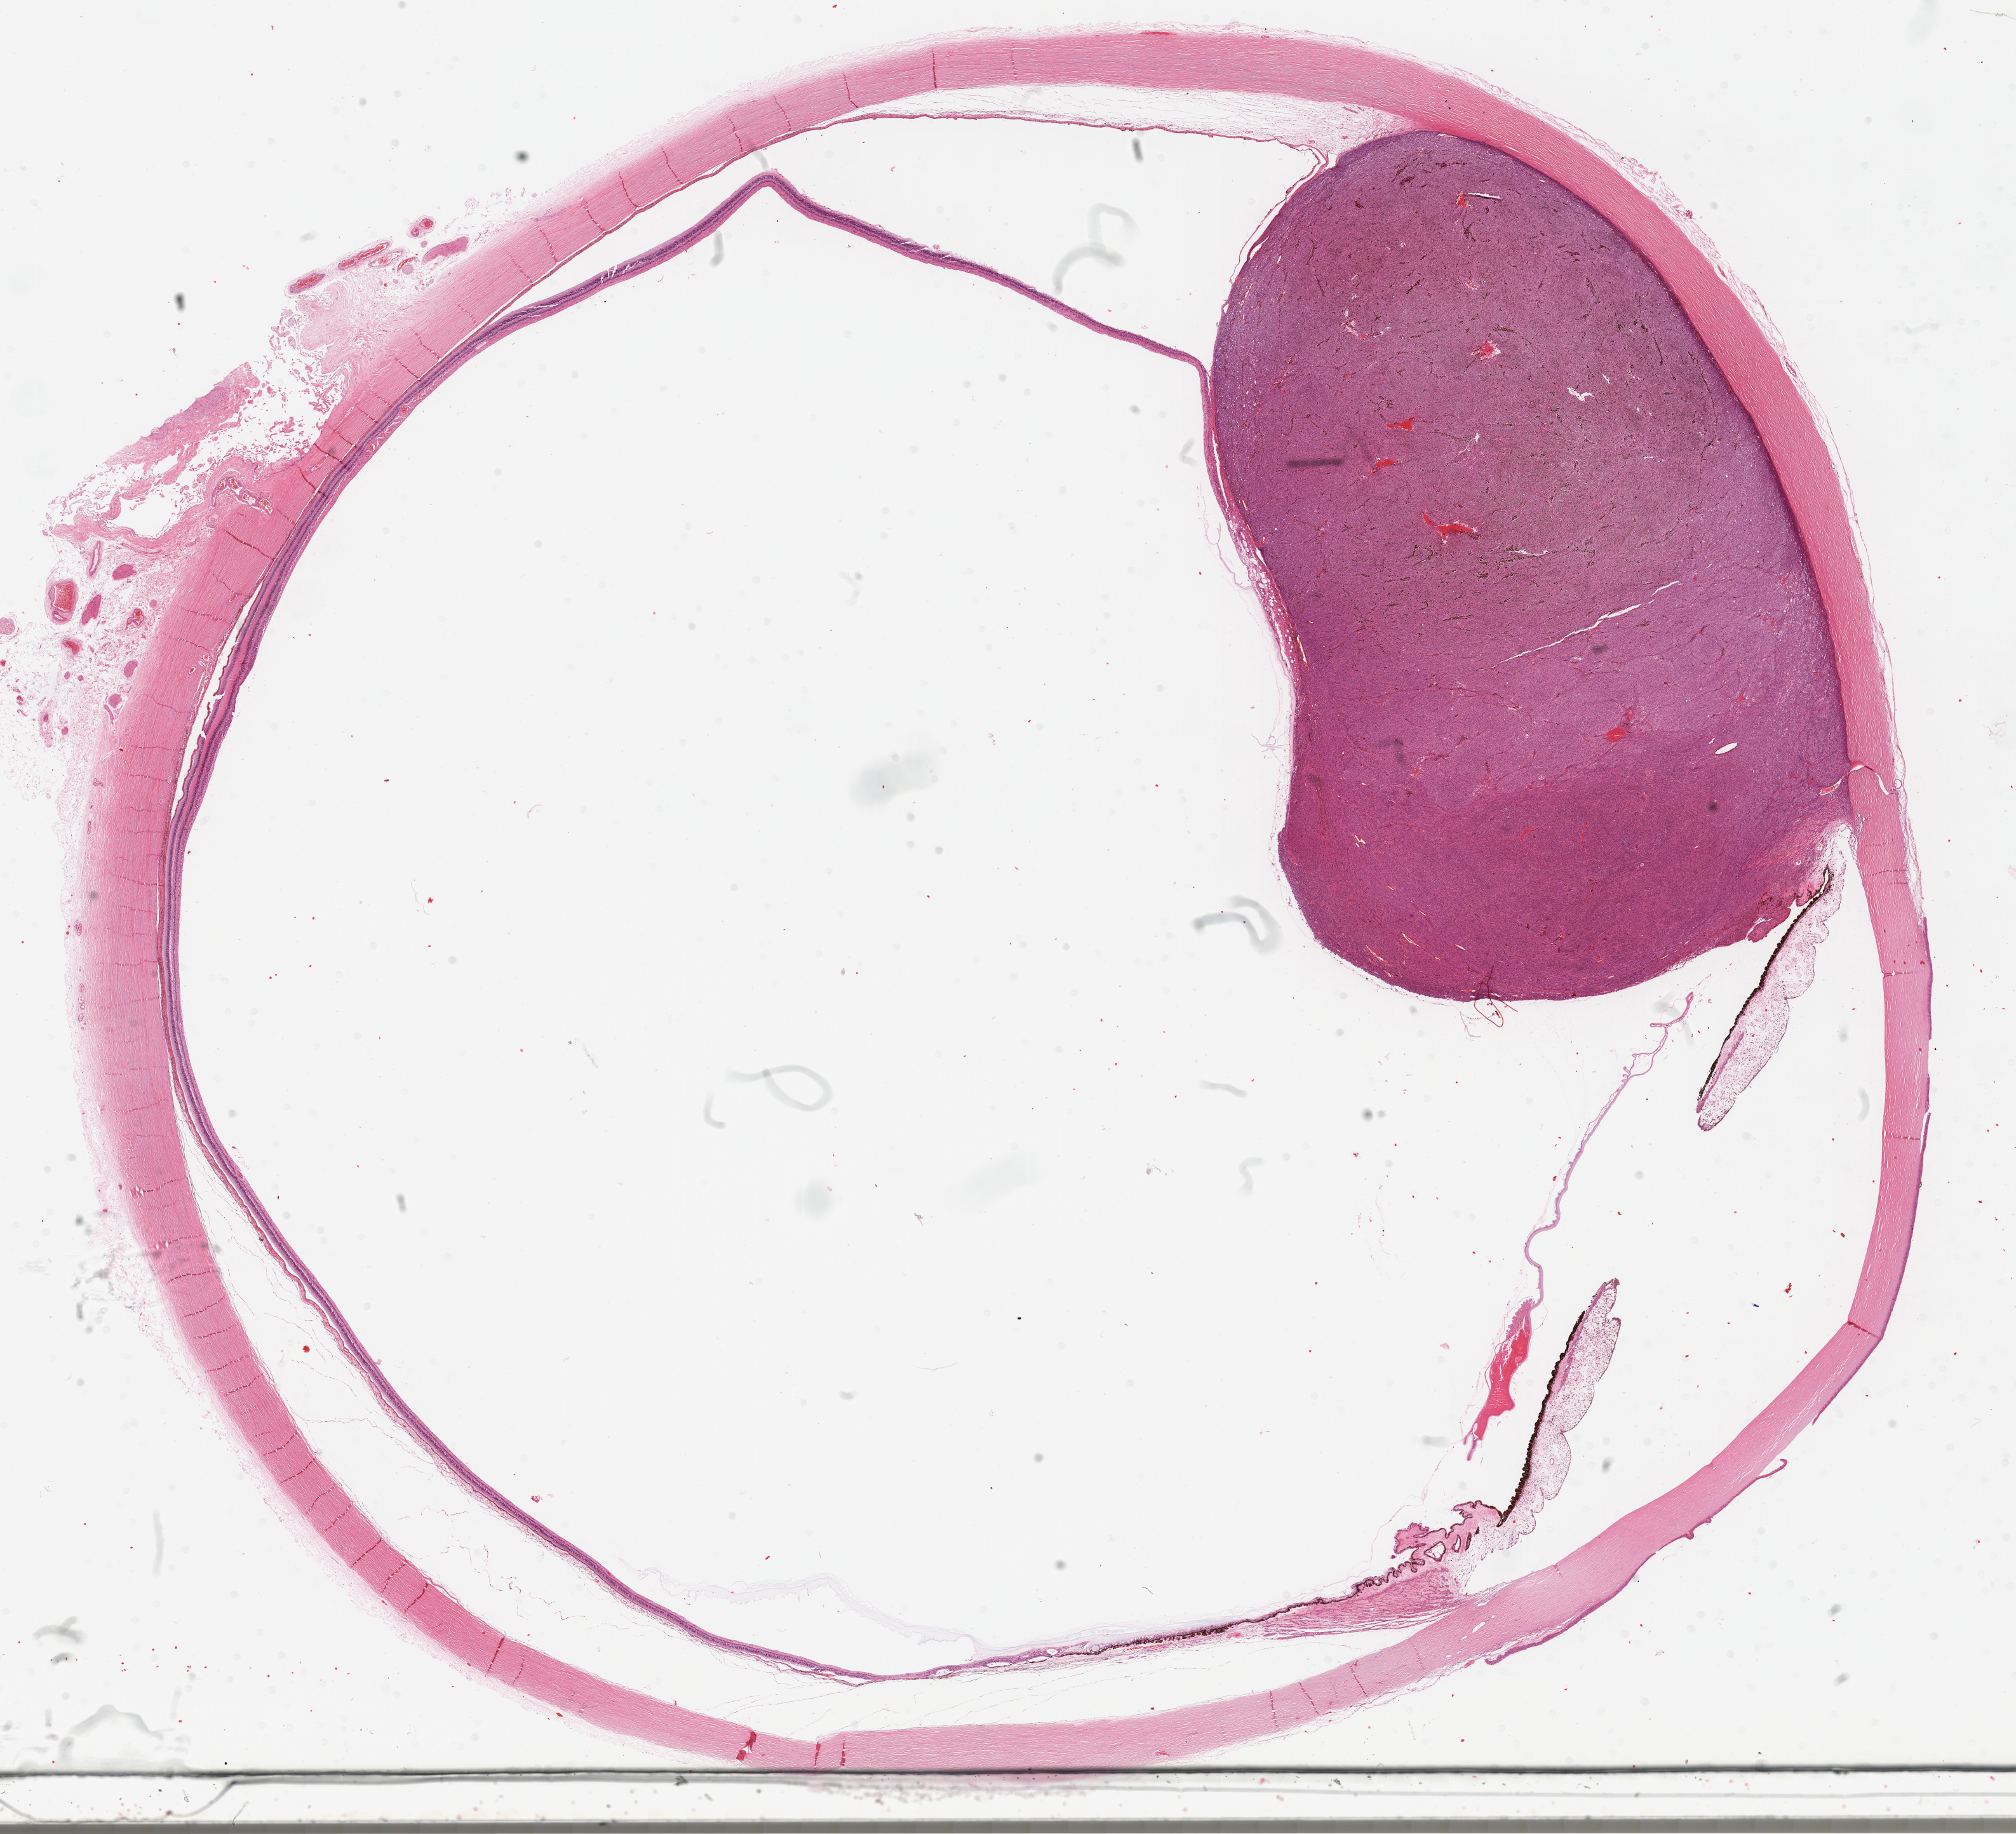
Whole-slide histology image, H&E, shown as a low-resolution overview of the whole scanned area (about 25.6 x 23.3 mm). Formalin-fixed paraffin-embedded (FFPE) diagnostic section. Sample: primary tumour, uvea. Female, age 83 years at initial diagnosis.
AJCC pathologic stage: IIA (7th edition). Diagnosis: Spindle cell melanoma, NOS (overlapping lesion of eye and adnexa).